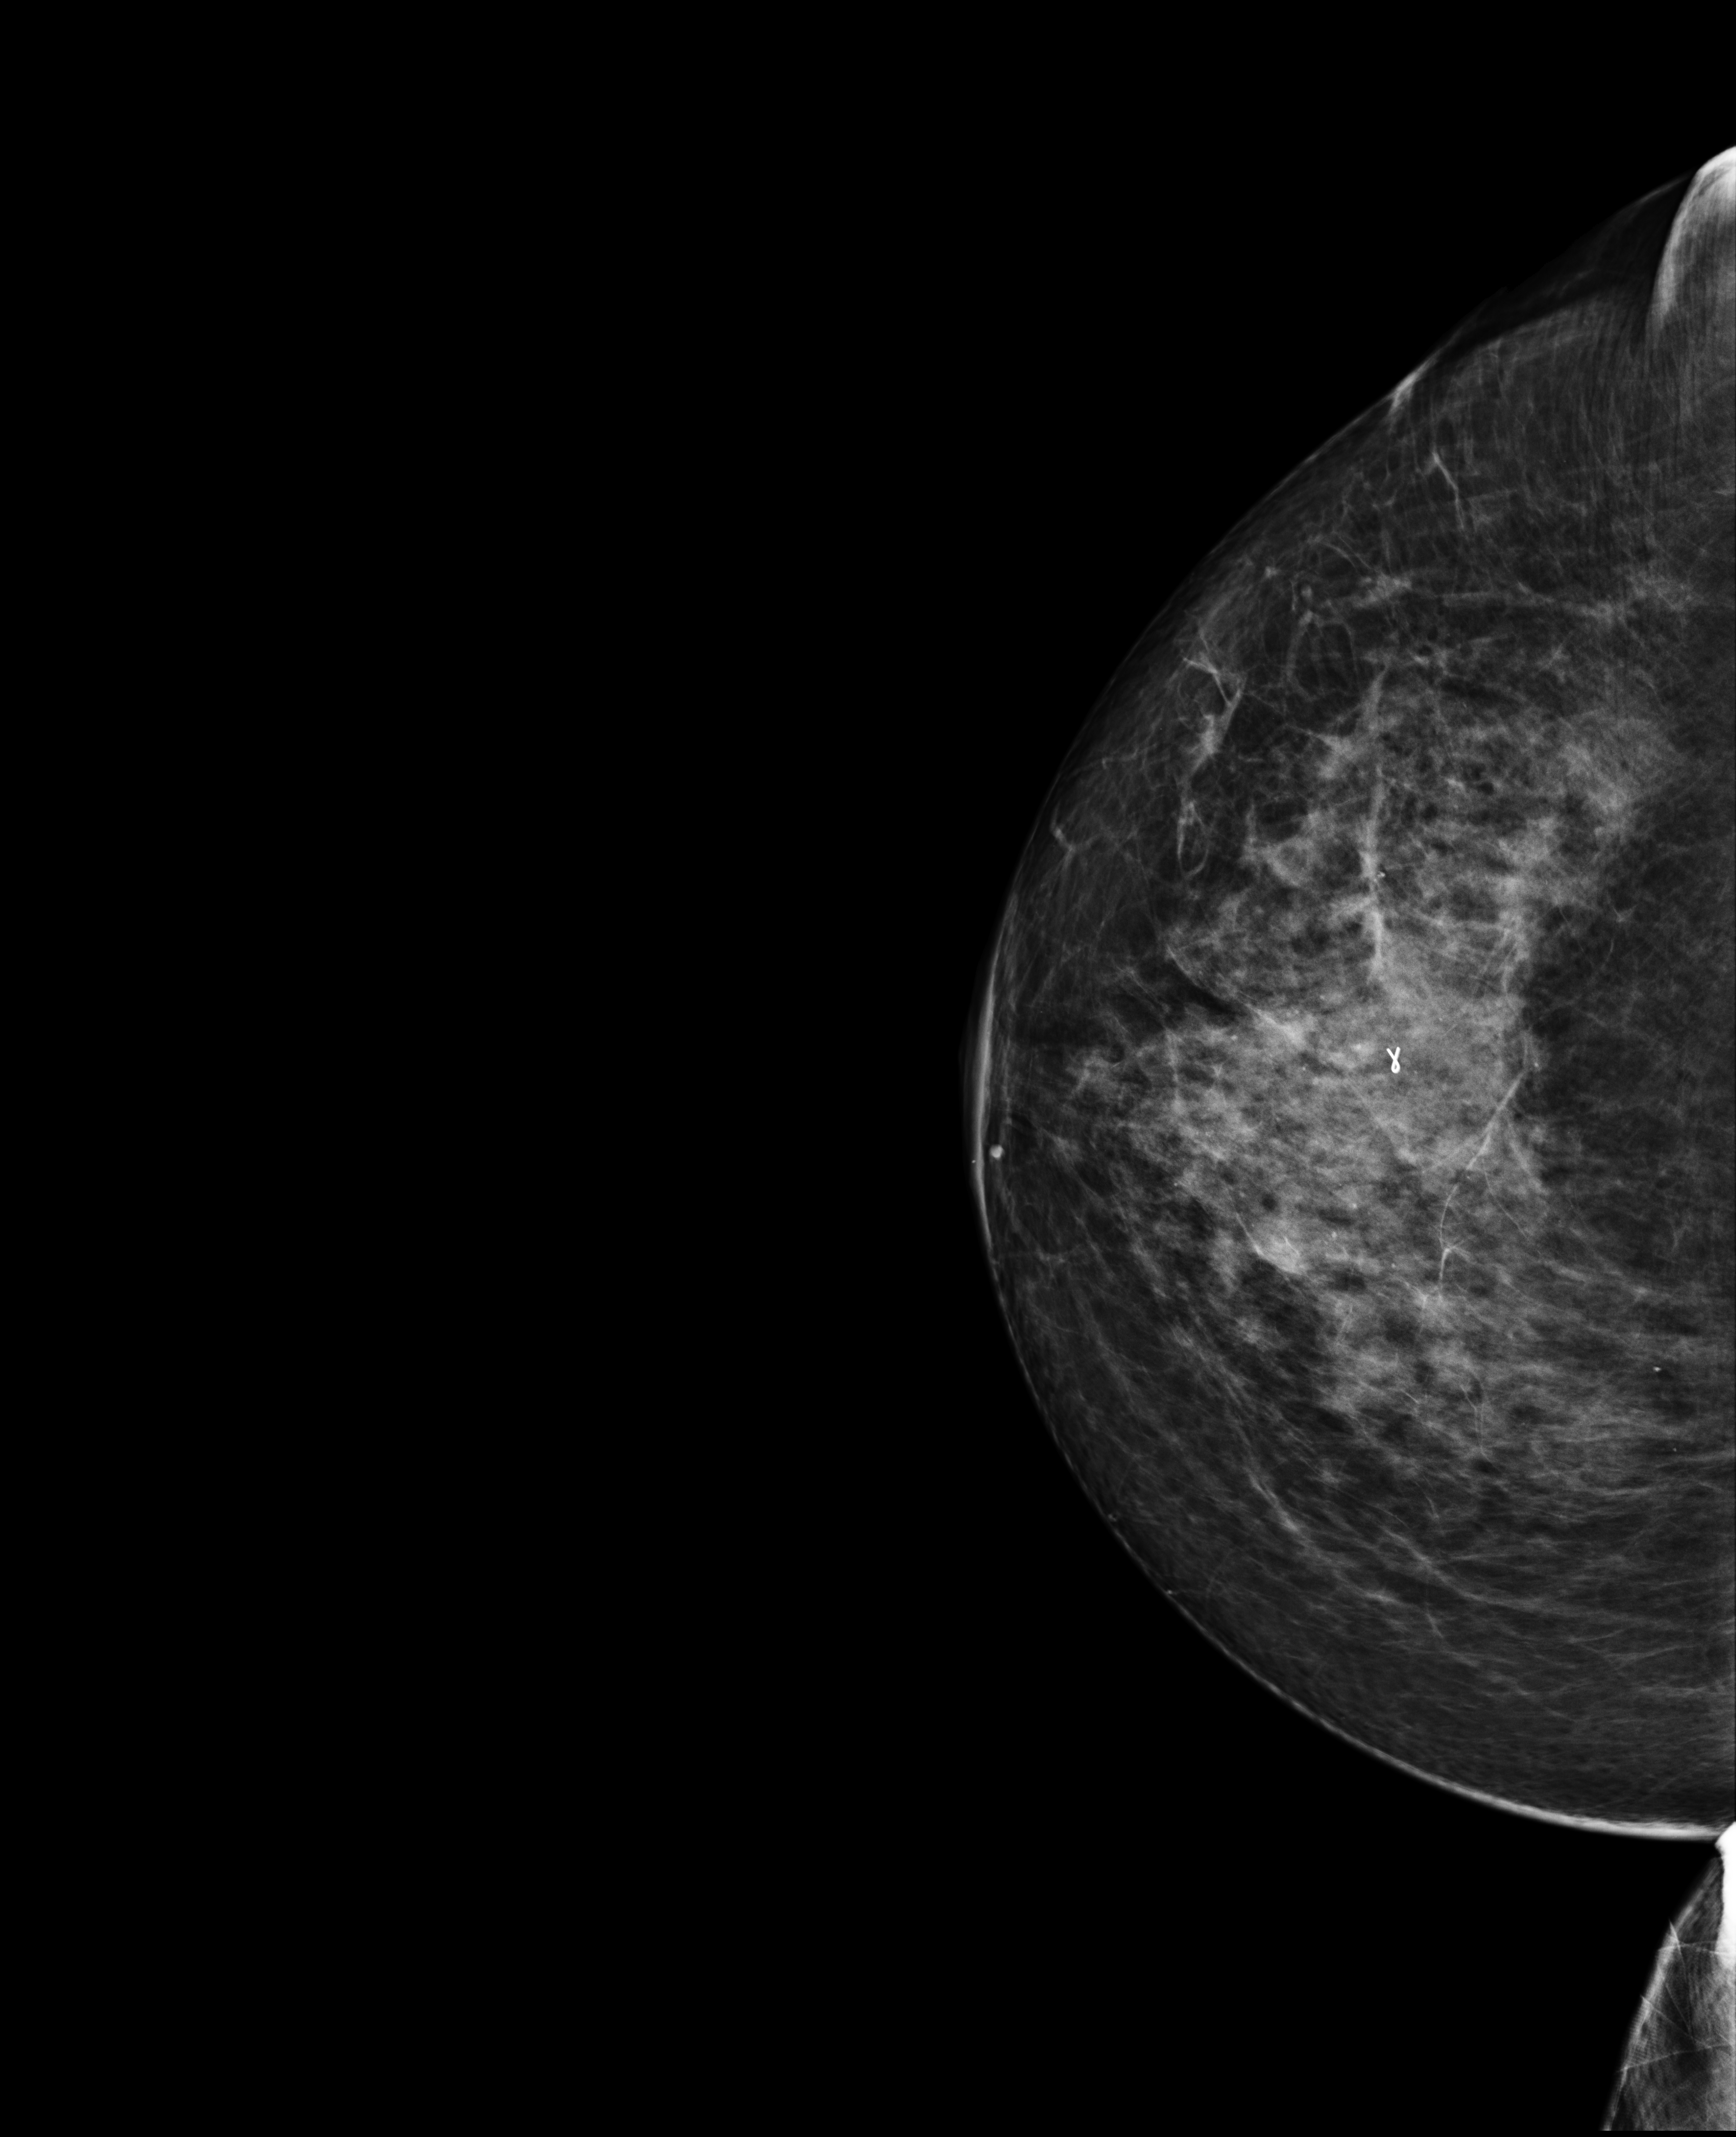
Diagnostic examination (additional views), compressed breast thickness 81 mm, system: Selenia Dimensions. Patient: female, 71 years.
Image type: full-field digital mammogram. Breast: right. Projection: CC view.